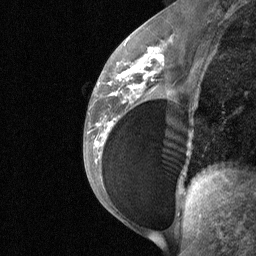
Breast MRI (dynamic contrast-enhanced), one sagittal slice. Slice 35 of 64 in the series (ordered by position). Dynamic contrast-enhanced study with each time point stored as its own series, time point 2 of 3 at this slice position (early post-contrast, ordered by acquisition time). 1.5 T. TE 4.8 ms, TR 27 ms. 256 × 256 image matrix, field of view 200 × 200 mm. Female patient, age 34 years. Case-level facts recorded for this patient, not image findings: setting: breast cancer imaged before/during neoadjuvant chemotherapy; receptor status: HR-positive, HER2-negative.
Annotated regions visible in this slice (semi-automatic segmentation, software-assisted and operator-edited):
- analysis volume of interest (the breast-tissue region the enhancement analysis was run in; not a lesion): bounding box (x1, y1, x2, y2) in pixels: (92, 50, 188, 185)
- tumour enhancement mask (voxels above the 90 % enhancement threshold inside the analysis volume of interest): (108, 50, 162, 126)